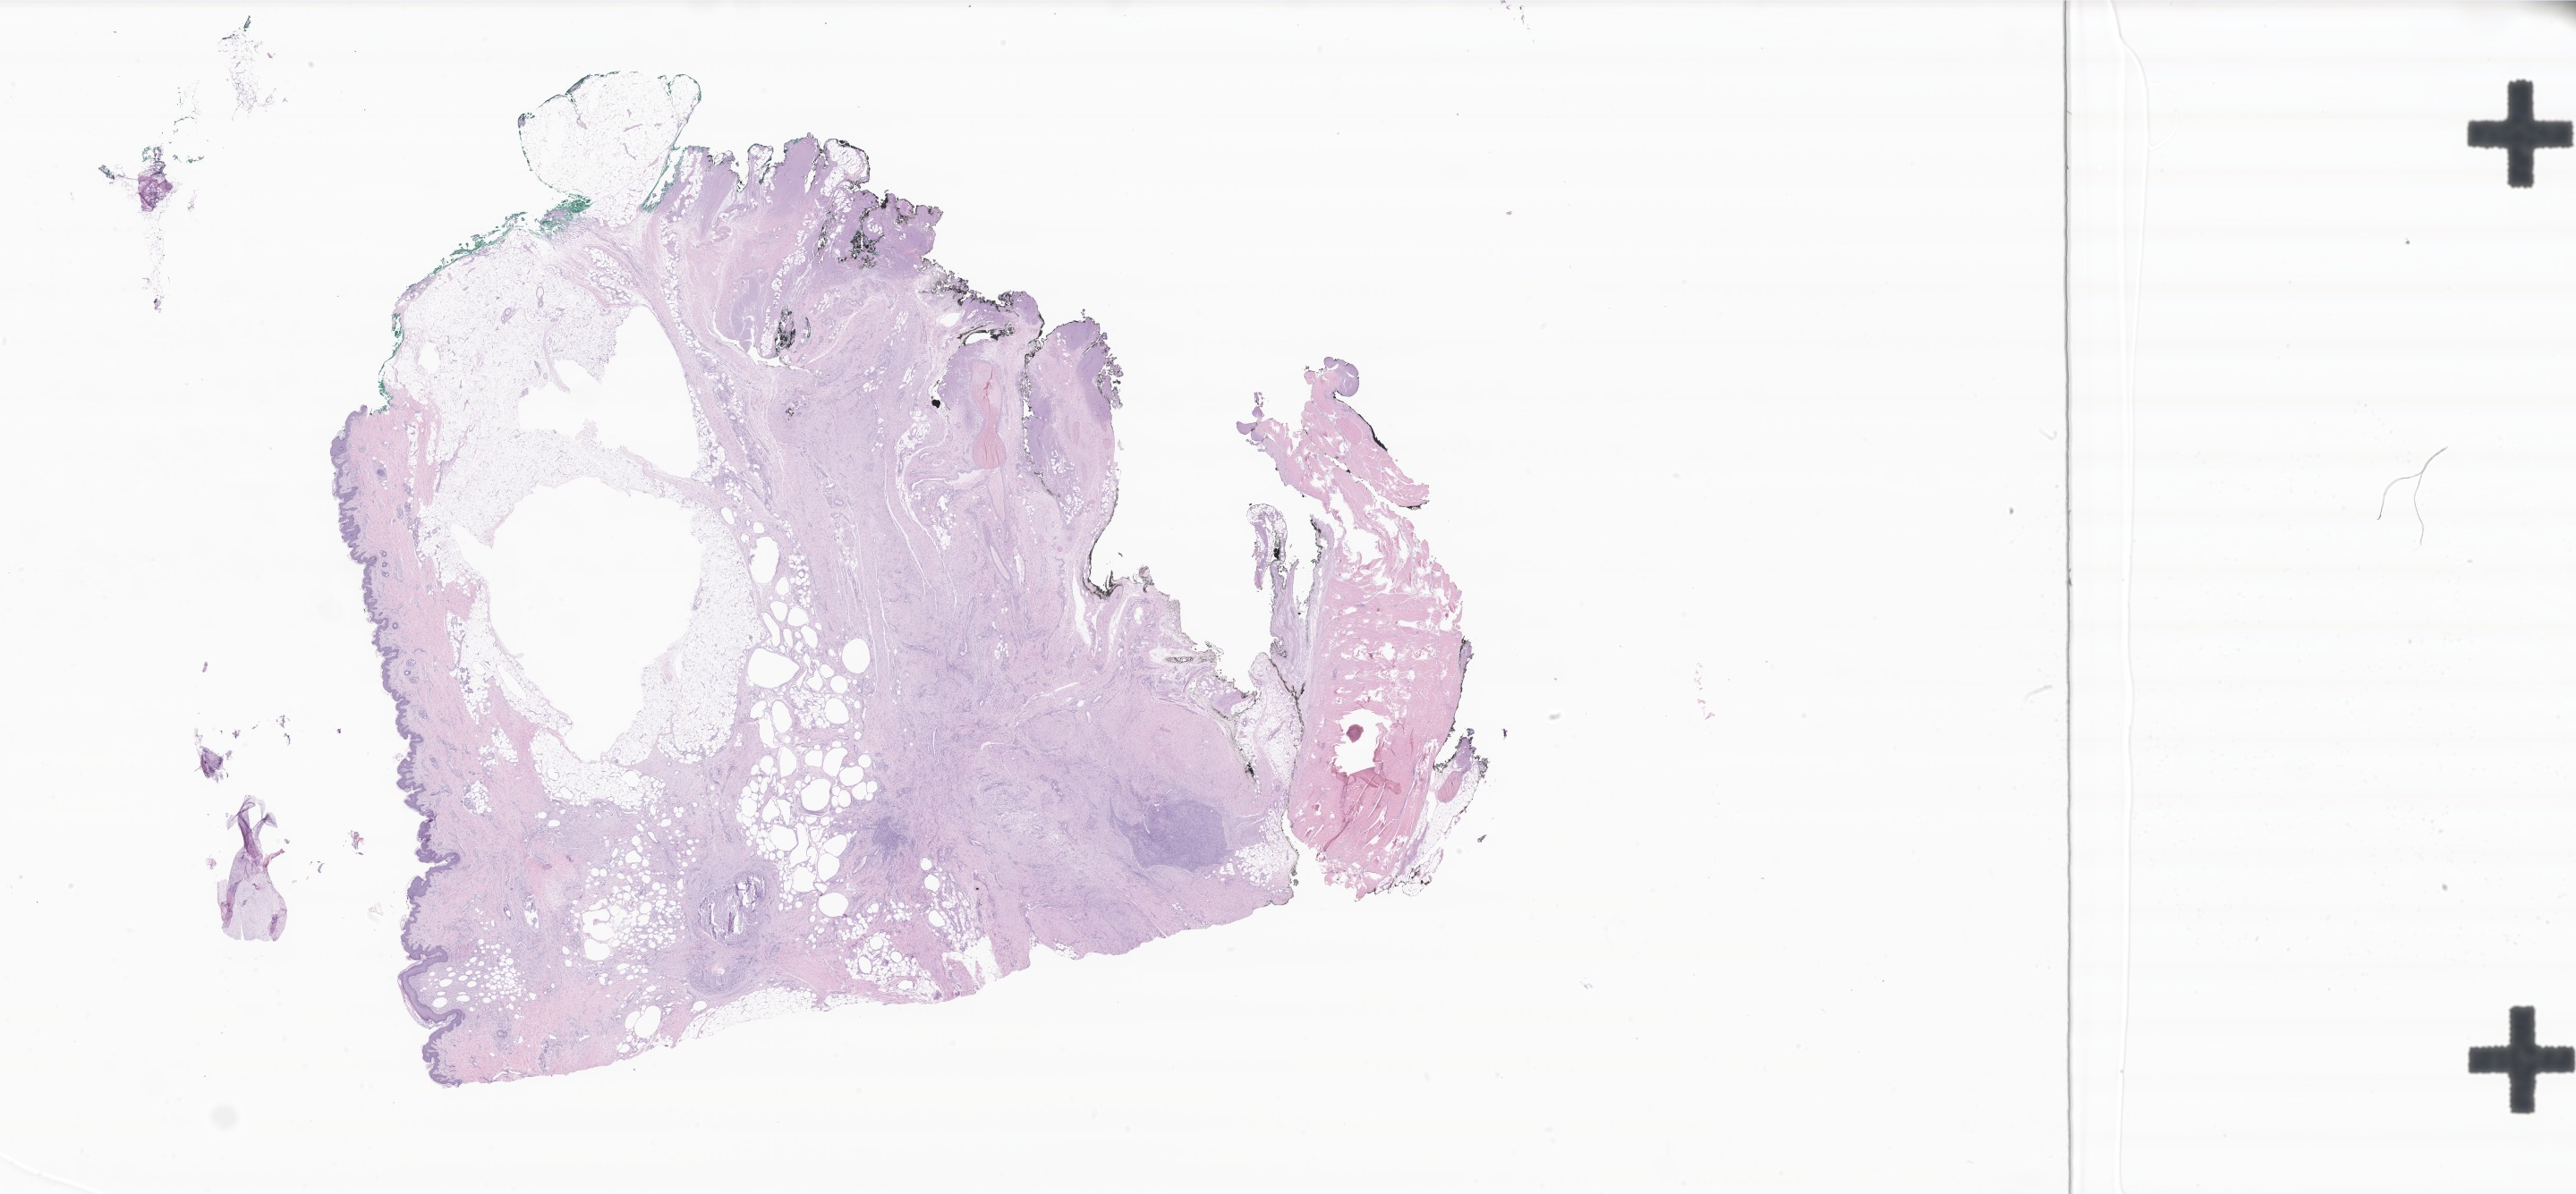
Haematoxylin and eosin whole-slide image of tumor tissue from the soft tissue of lower extremity, whole scanned area (about 48.6 x 22.5 mm) shown as a low-resolution overview; FFPE section. Patient: male, age 83 months (6 years 11 months).
- recorded diagnosis: Synovial sarcoma, spindle cell
- tissue or organ of origin (case record): connective, subcutaneous and other soft tissues of lower limb and hip